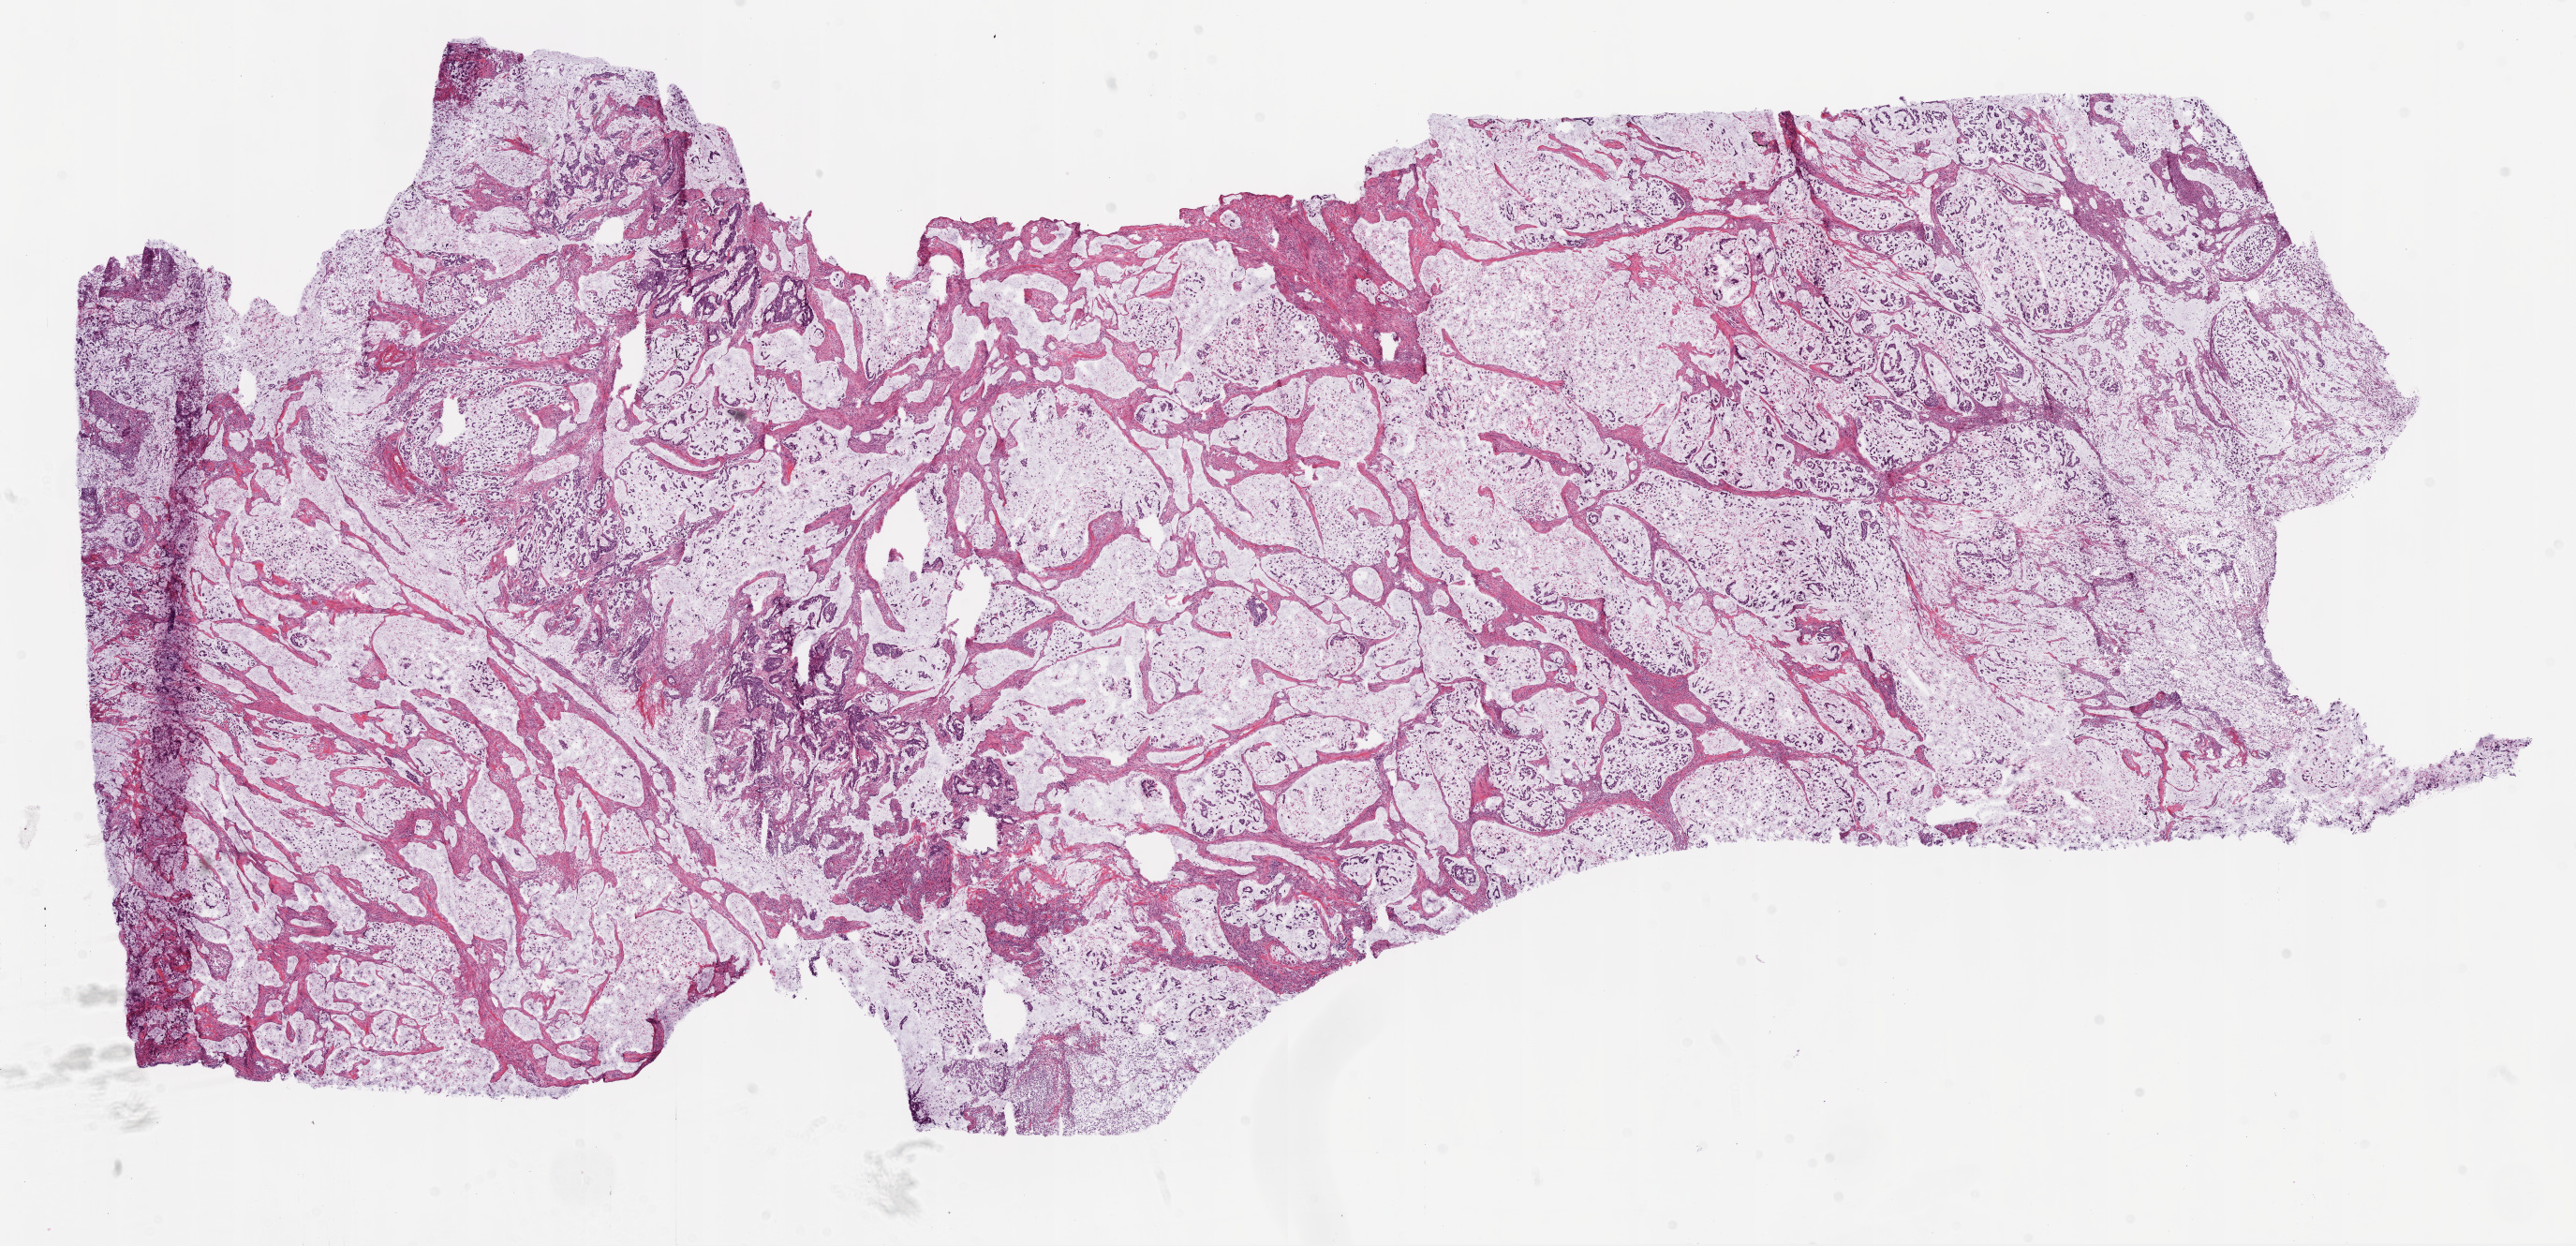
Digitized Hematoxylin and eosin (H&E) stained tissue section (whole slide), whole scanned area (about 22.1 x 10.7 mm) shown as a low-resolution overview; frozen section from the bottom of the tissue portion; sample: primary tumour, rectum. Patient: male, age at initial diagnosis 54 years. Composition of this section per pathologist review: tumour cells 90%, tumour nuclei 80%, normal cells 0%, stromal cells 10%, necrosis 0%.
AJCC pathologic stage: IIA. Diagnosis: Mucinous adenocarcinoma (rectosigmoid junction). Lymph nodes positive (case pathology): 0 of 32 examined. TNM: T3 N0 M0.